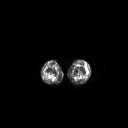
FDG PET of an extremity soft-tissue mass (from a PET/CT study), one axial slice. Slice 164 of 223 in the series (ordered by position). 3.27 mm slice thickness. 128 × 128 image matrix, field of view 700 × 700 mm. Female patient, age 16 years. From the clinical record (not read from this slice): histological type: spindle cell suggestive of biphasic synovial sarcoma; grade: intermediate; site of the primary tumour: left knee.
Structures marked on this image (expert contour drawn on MRI and transferred to this co-registered scan by the dataset authors):
- gross tumour volume including surrounding oedema: bounding box [x1, y1, x2, y2] px = [86, 68, 88, 71]